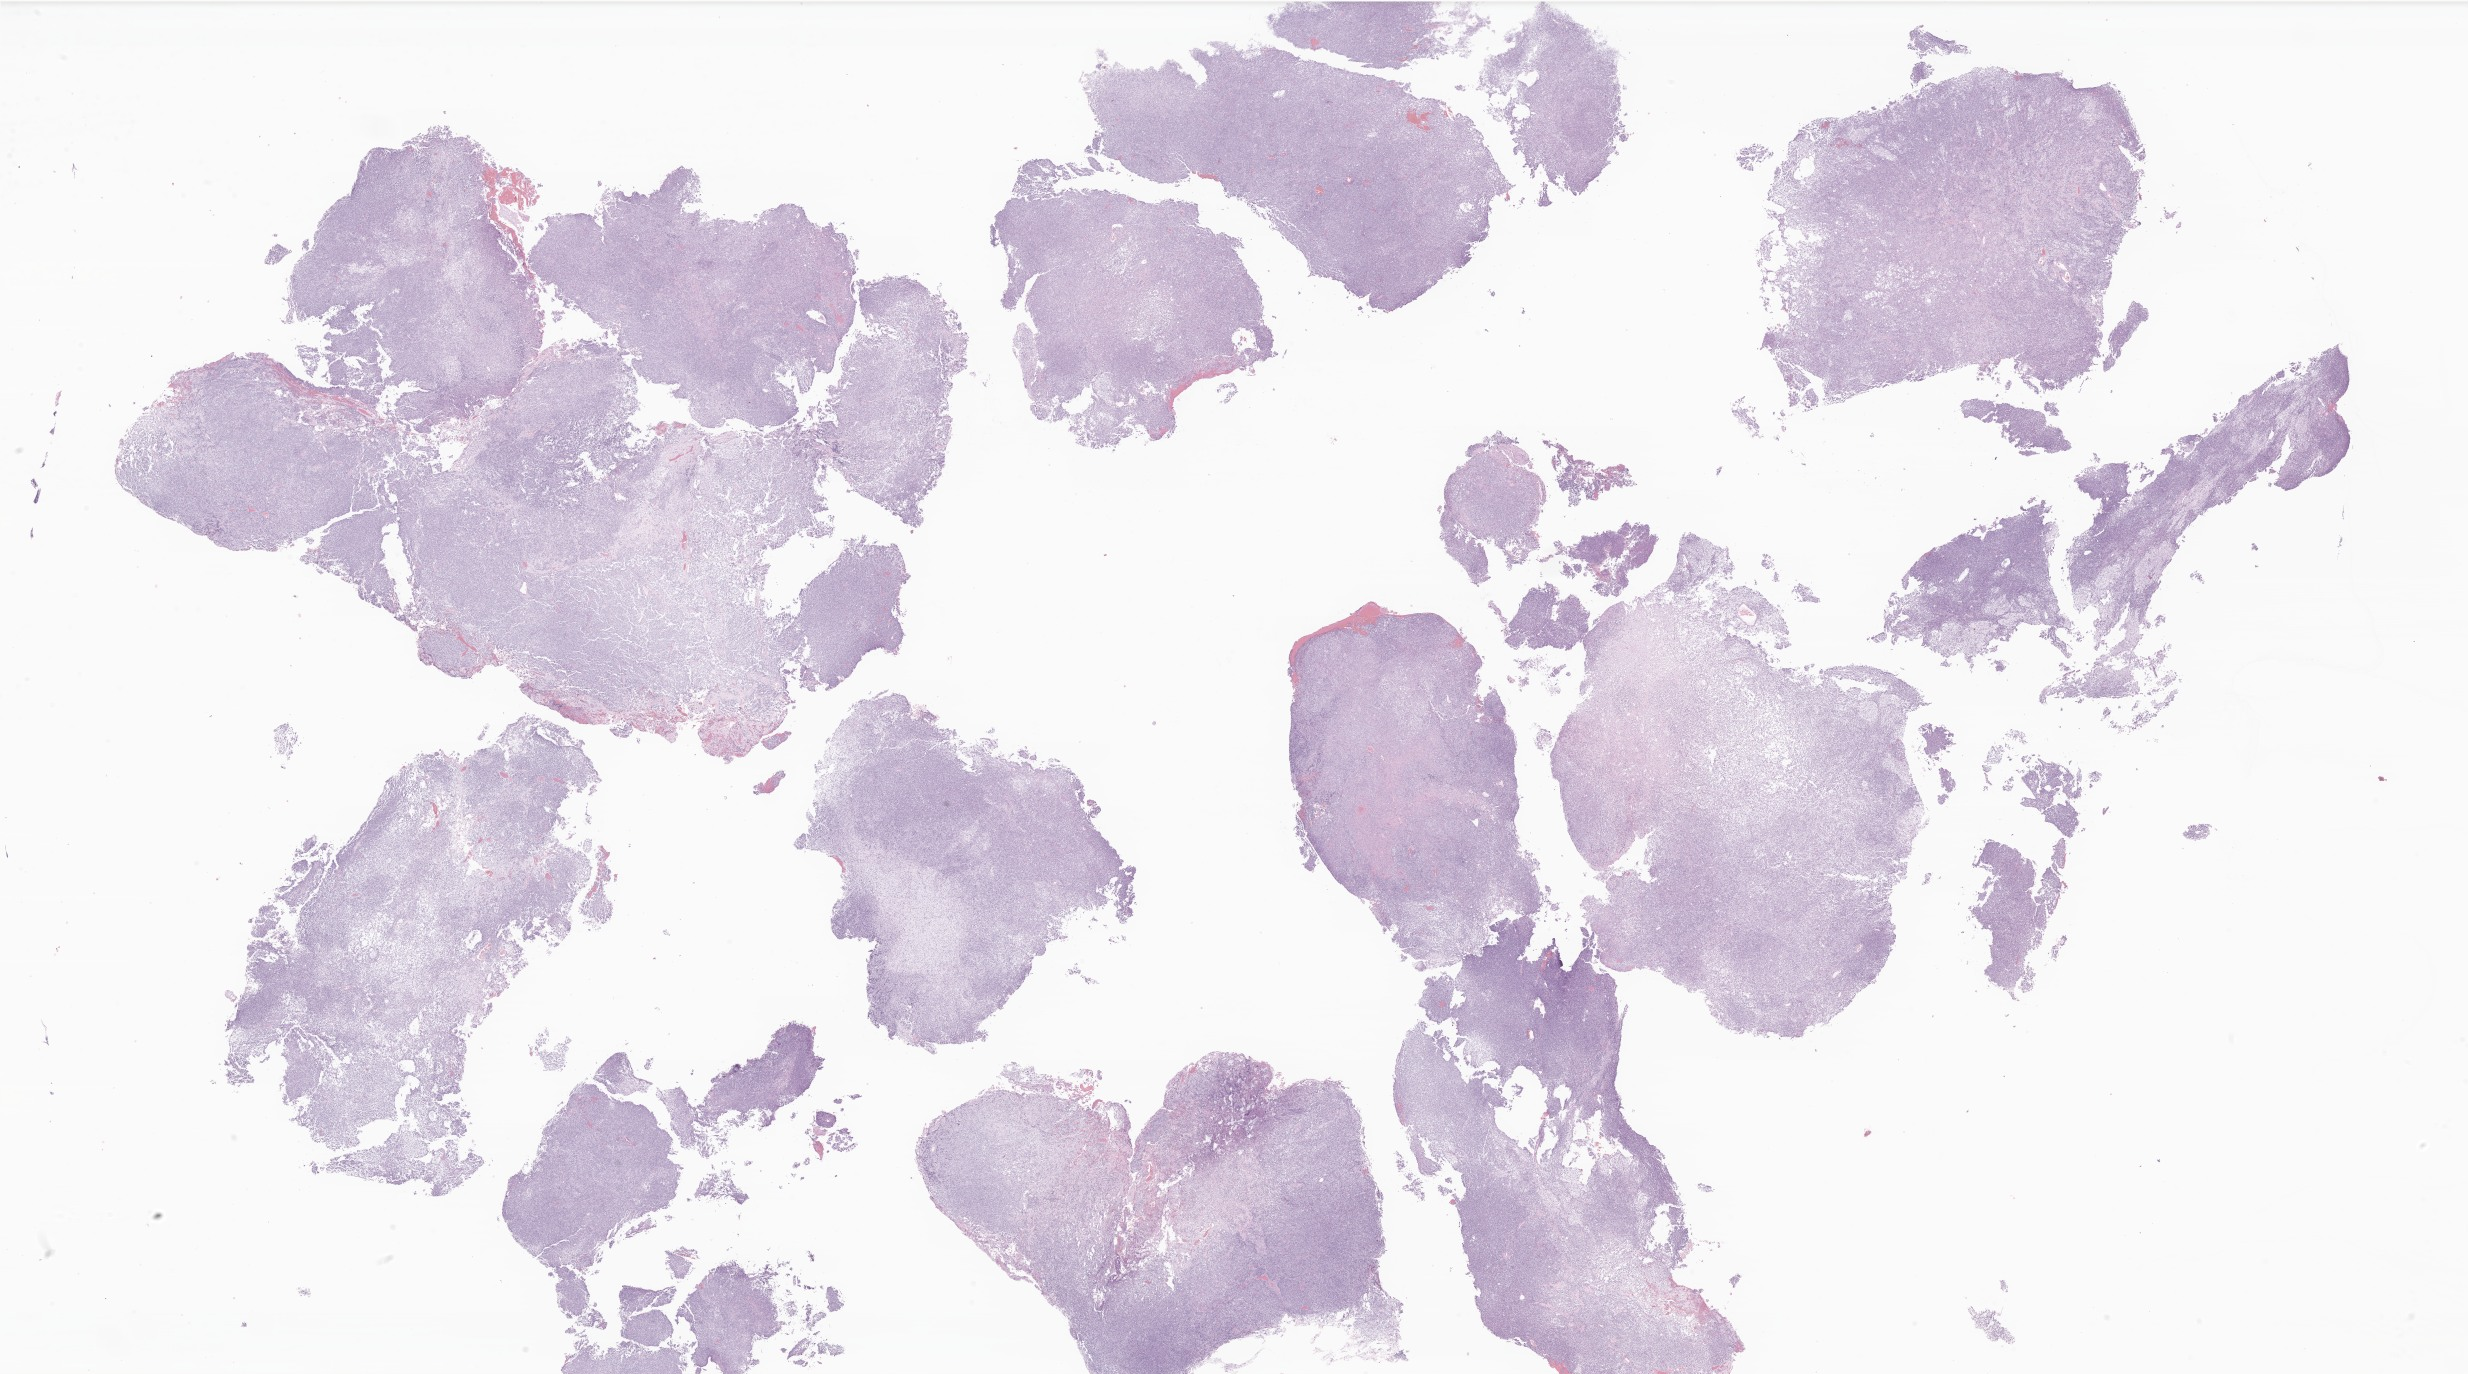
Whole-slide image, hematoxylin and eosin (H&E) stain of tumor tissue from the brain — a low-resolution overview of the entire scanned area, about 41.6 x 23.2 mm, formalin-fixed, paraffin-embedded (FFPE) tissue. Male patient, age 871 days (about 2.4 years).
• diagnosis: Atypical teratoid/rhabdoid tumor